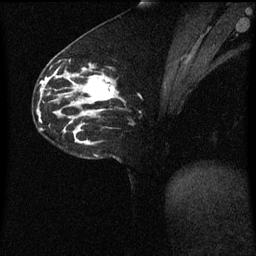
Breast MRI (dynamic contrast-enhanced), one sagittal slice. Position 26 of 60 along the scan axis. Dynamic contrast-enhanced series, image 2 of 3 at this slice position (ordered by acquisition). 1.5 T. TE 4.2 ms, TR 8.4 ms. 2 mm slice thickness. 256 × 256 image matrix. Female patient, age 33 years. From the clinical record (not read from this slice): setting: breast cancer imaged before/during neoadjuvant chemotherapy; receptor status: triple-negative.
Annotated regions visible in this slice (semi-automatic segmentation, software-assisted and operator-edited):
- analysis volume of interest (the breast-tissue region the enhancement analysis was run in; not a lesion): bounding box [x1, y1, x2, y2] px = [76, 64, 122, 113]
- tumour enhancement mask (voxels above the 70 % enhancement threshold inside the analysis volume of interest): [83, 76, 114, 101]